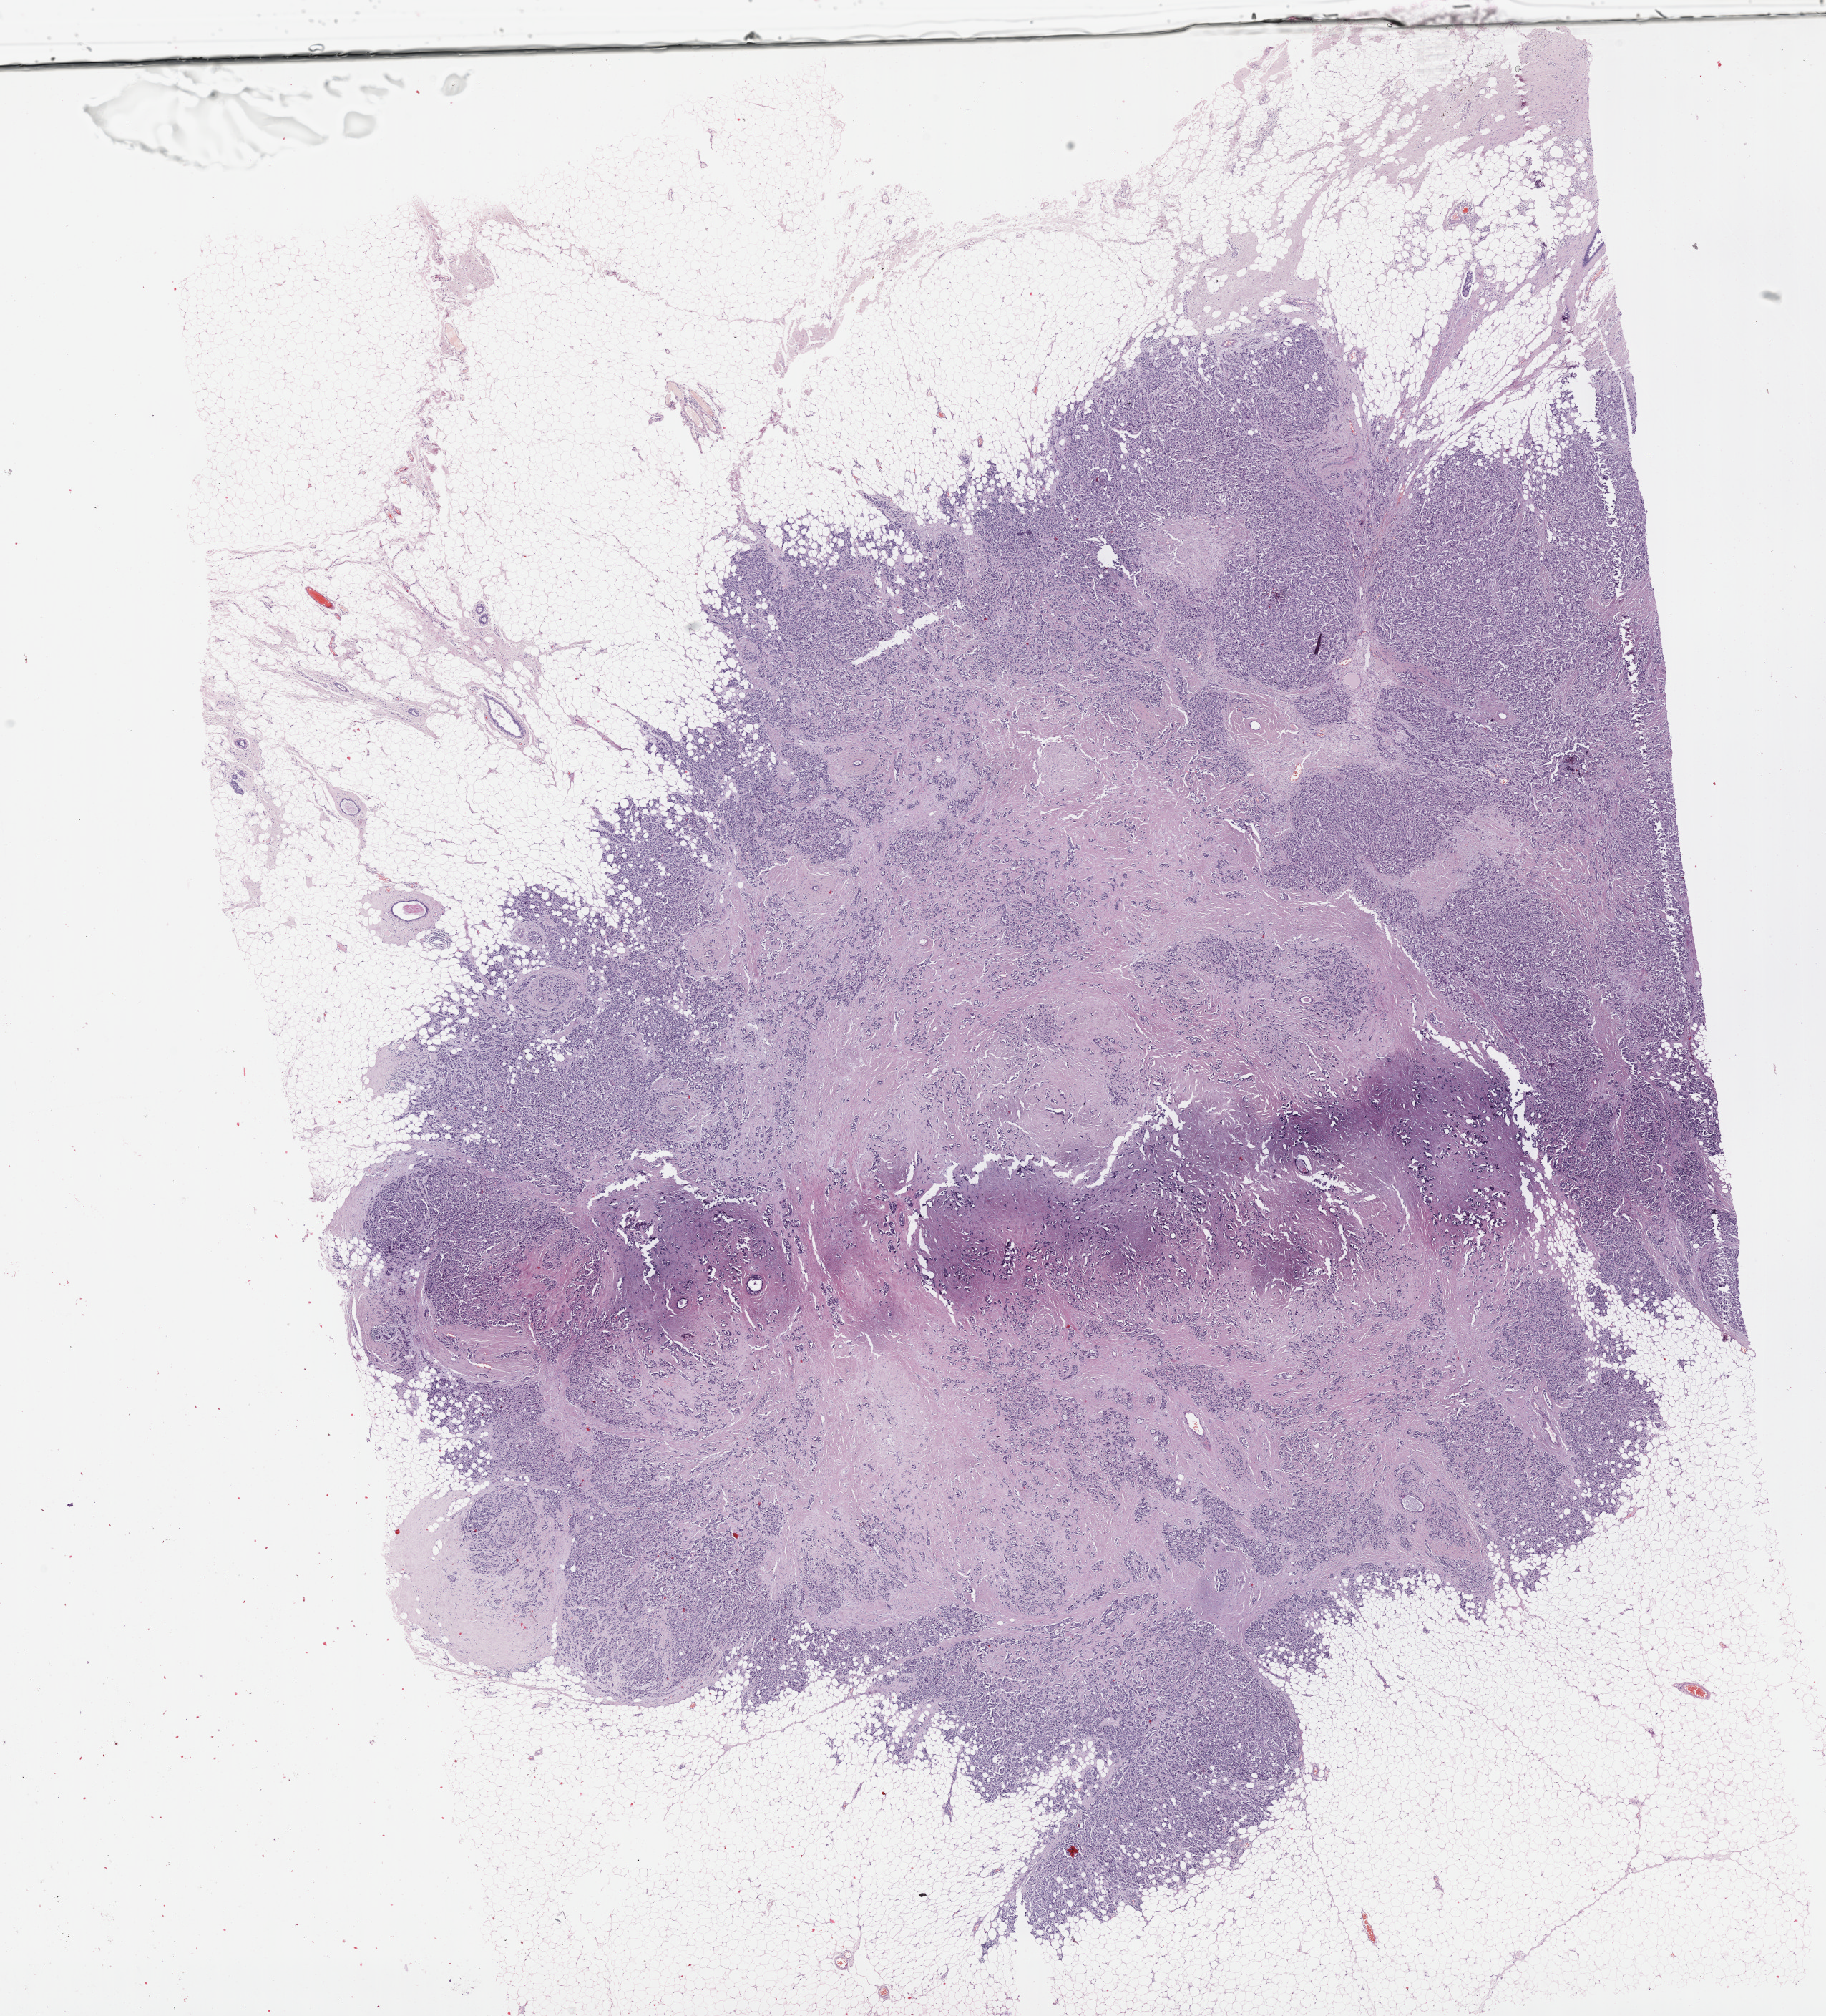
Digitized H&E tissue section (whole slide), low-resolution overview of the scanned area, about 20.6 x 22.8 mm, formalin-fixed paraffin-embedded (FFPE) diagnostic section, breast, primary tumour sample. Patient: female, age at initial diagnosis 56 years.
Lymph nodes positive (case pathology): 2 of 7 examined. Laterality: right. AJCC pathologic stage: IIB (7th edition). Diagnosis: Infiltrating duct carcinoma, NOS.